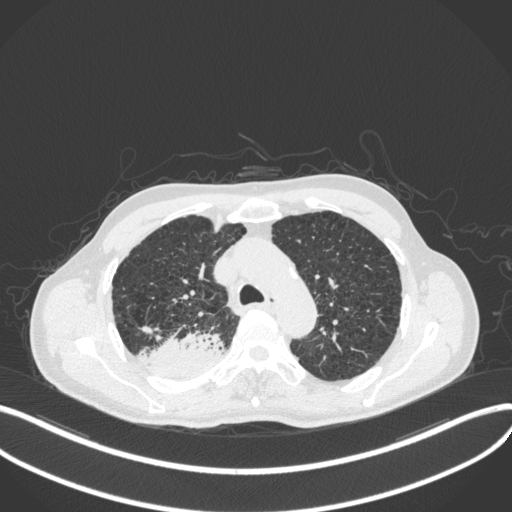
Chest CT, one axial slice. Position 327 of 423 along the scan axis. Reconstruction kernel B31f. Lung window (W 1500 / L -600 HU). 1 mm slice thickness. 512 × 512 image matrix. Male patient, age 79 years. Case-level facts recorded for this patient, not image findings: clinical TNM (as recorded): T3 N0 M0.
Outlined on this slice (rectangle marked by the reading radiologist):
- lung tumour (recorded histology: adenocarcinoma): bounding box [x1, y1, x2, y2] px = [149, 329, 224, 382]